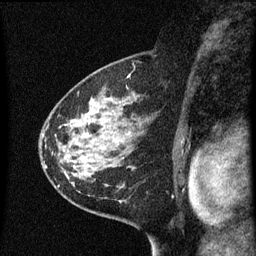
Breast MRI (dynamic contrast-enhanced), one sagittal slice. Position 37 of 60 along the scan axis. Dynamic contrast-enhanced series, image 2 of 3 at this slice position (ordered by acquisition). 1.5 T. TE 4.2 ms, TR 8 ms. 256 × 256 image matrix. Patient: female, 60 years.
Structures marked on this image (semi-automatic segmentation, software-assisted and operator-edited):
- analysis volume of interest (the breast-tissue region the enhancement analysis was run in; not a lesion): bounding box <48,82,155,183> (left, top, right, bottom; pixels)
- tumour enhancement mask (voxels above the 70 % enhancement threshold inside the analysis volume of interest): <75,98,110,169>